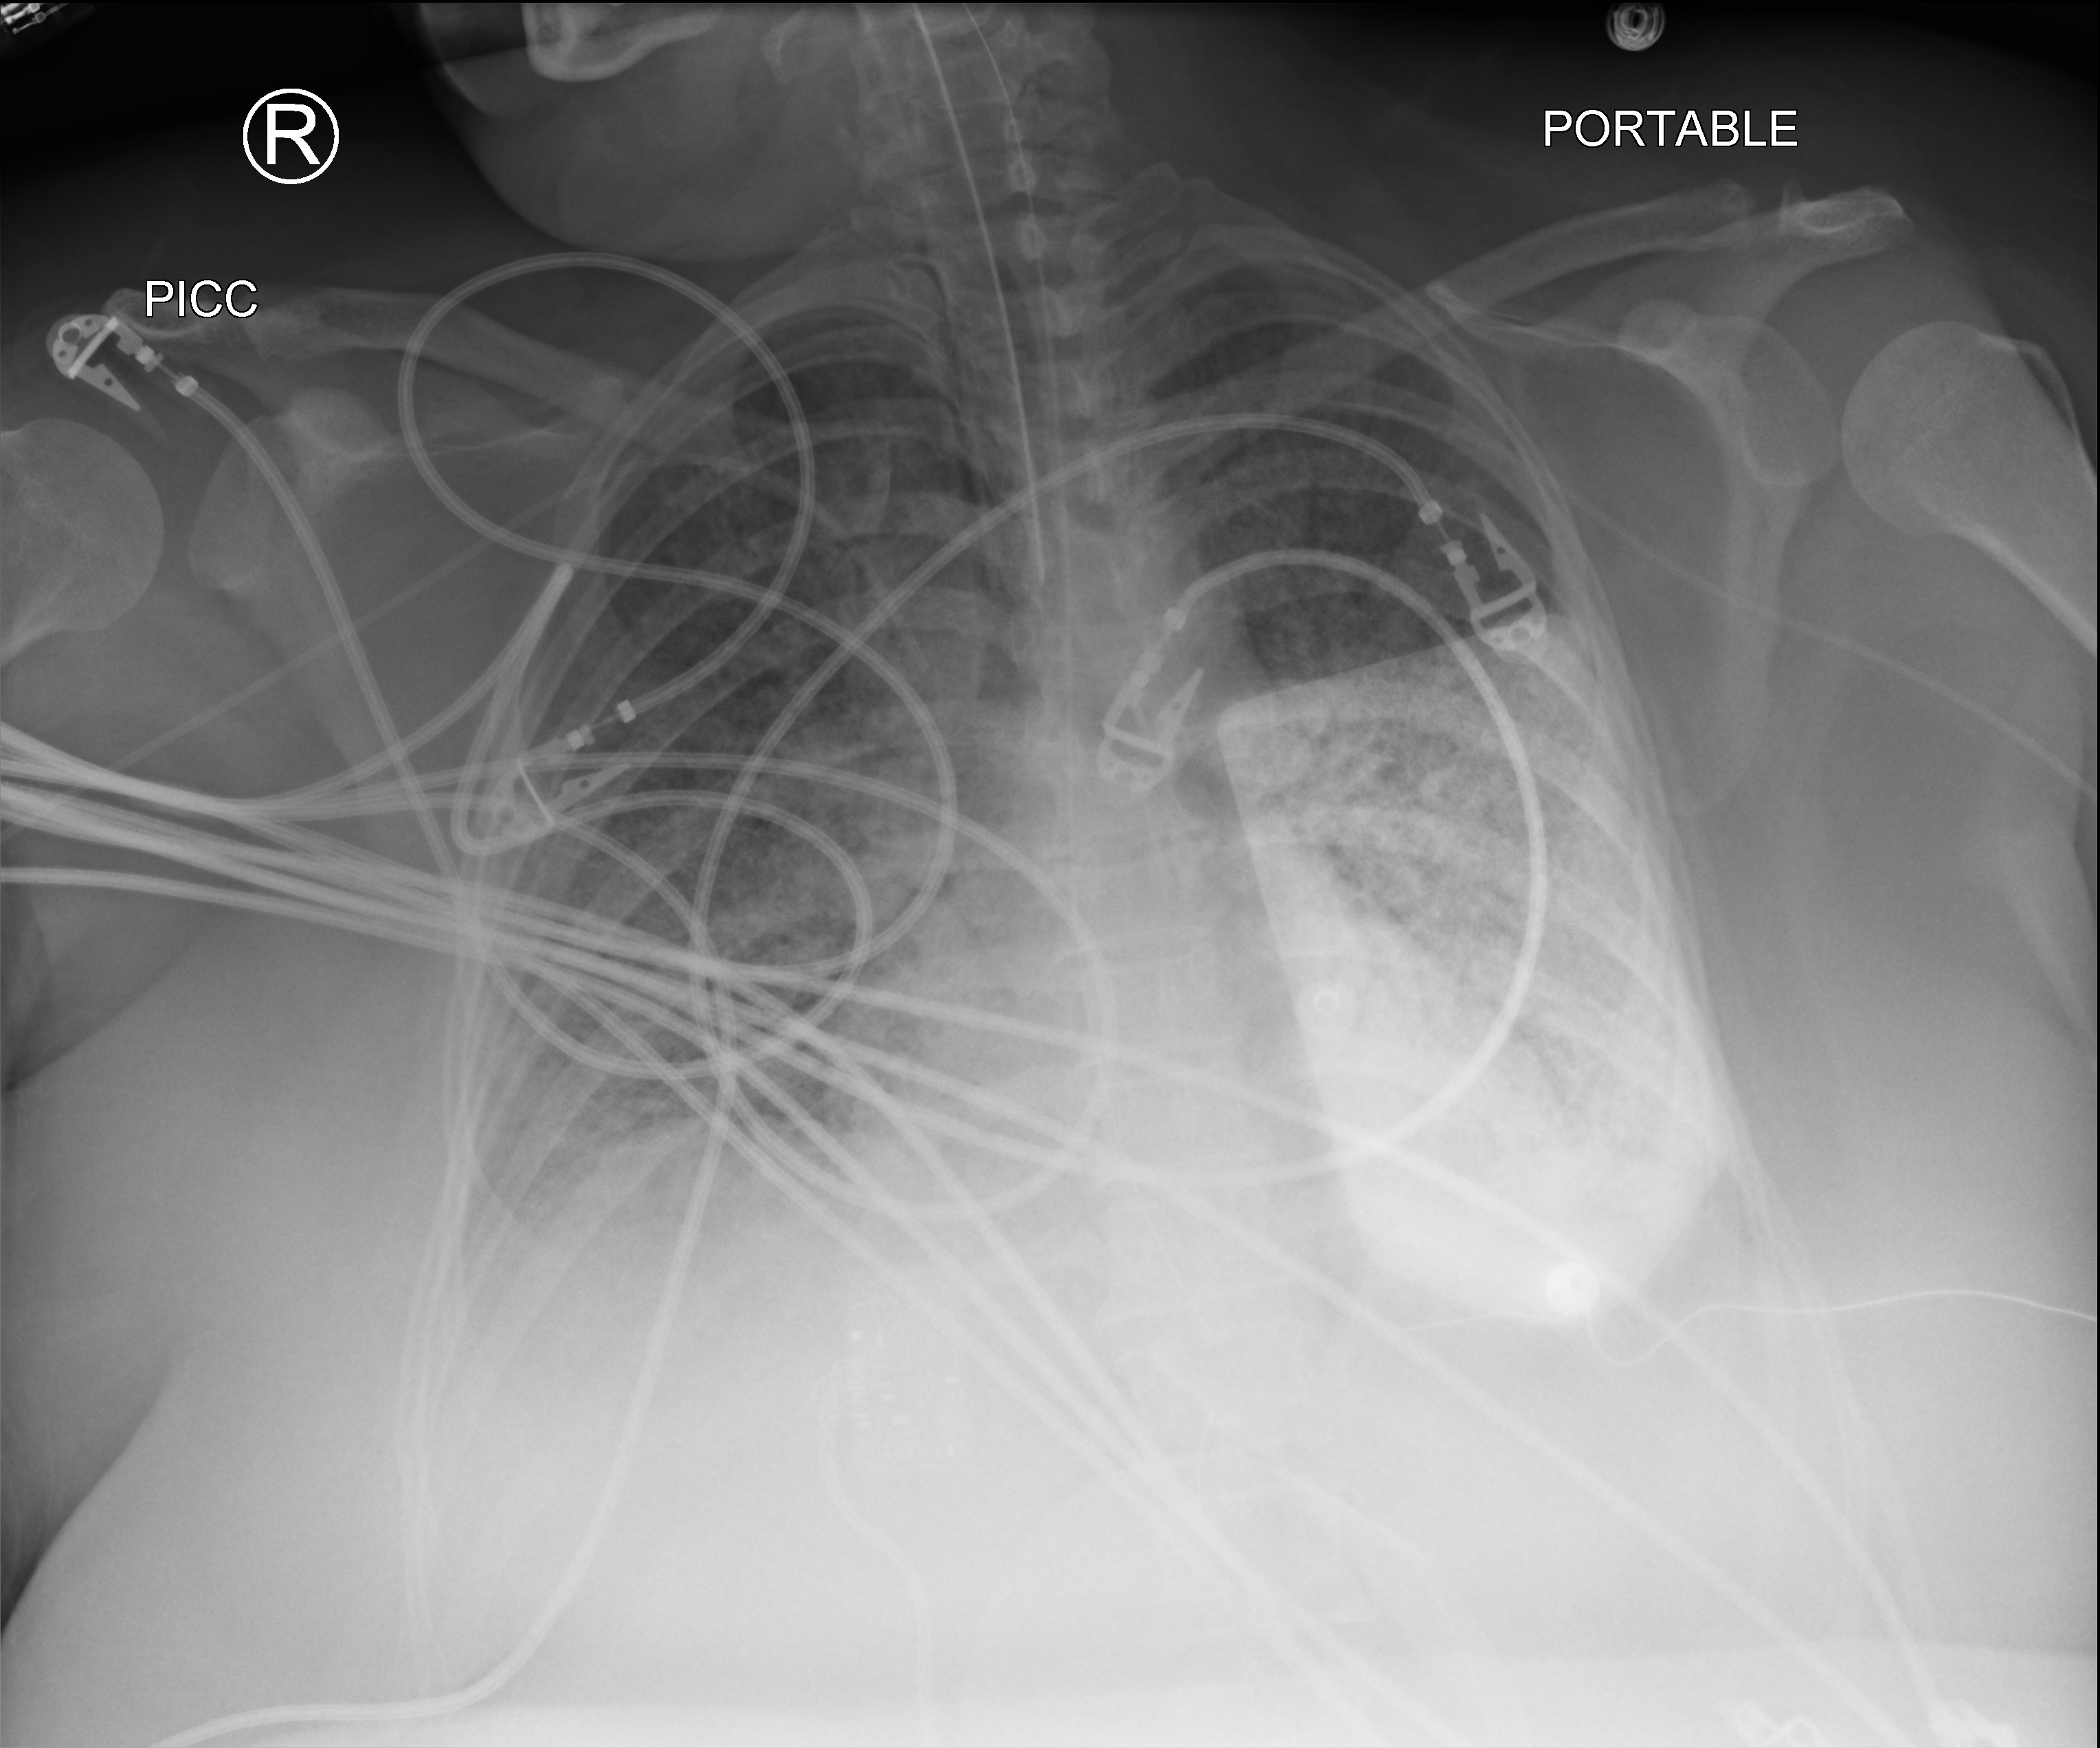
Portable chest radiograph, anteroposterior (AP) projection. Female patient hospitalised with COVID-19, age 18–59 years.
Admission-level facts for this patient (not findings on this image; timing relative to this image not recorded): hypertension (admission record): yes; mechanically ventilated during this hospital stay: yes; admitted to intensive care during this hospital stay: yes.